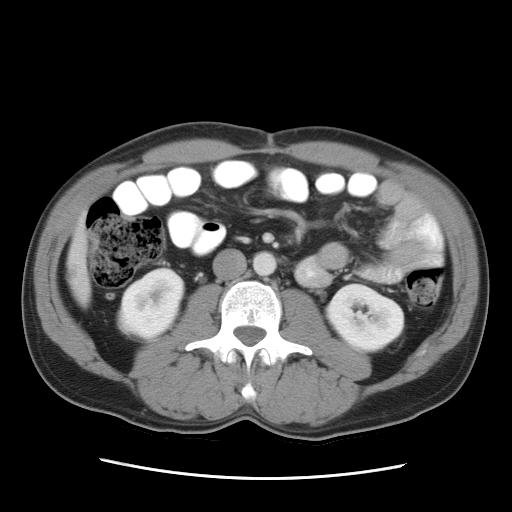
Contrast-enhanced abdominal CT, one axial slice; position 7 of 34 along the scan axis; 120 kVp; soft-tissue window (W 400 / L 40 HU); 7.5 mm slice thickness; 512 × 512 image matrix, field of view 360 × 360 mm. Male patient, age 40 years. From the clinical record (not read from this slice): diagnosis: colorectal cancer liver metastases, imaged before liver resection; multiple liver metastases: yes; largest metastasis: 1.5 cm.
Structures marked on this image (outlined manually by an expert reader):
- liver: bounding box [x1, y1, x2, y2] px = [67, 222, 92, 303]
- liver metastasis: [66, 261, 80, 281]